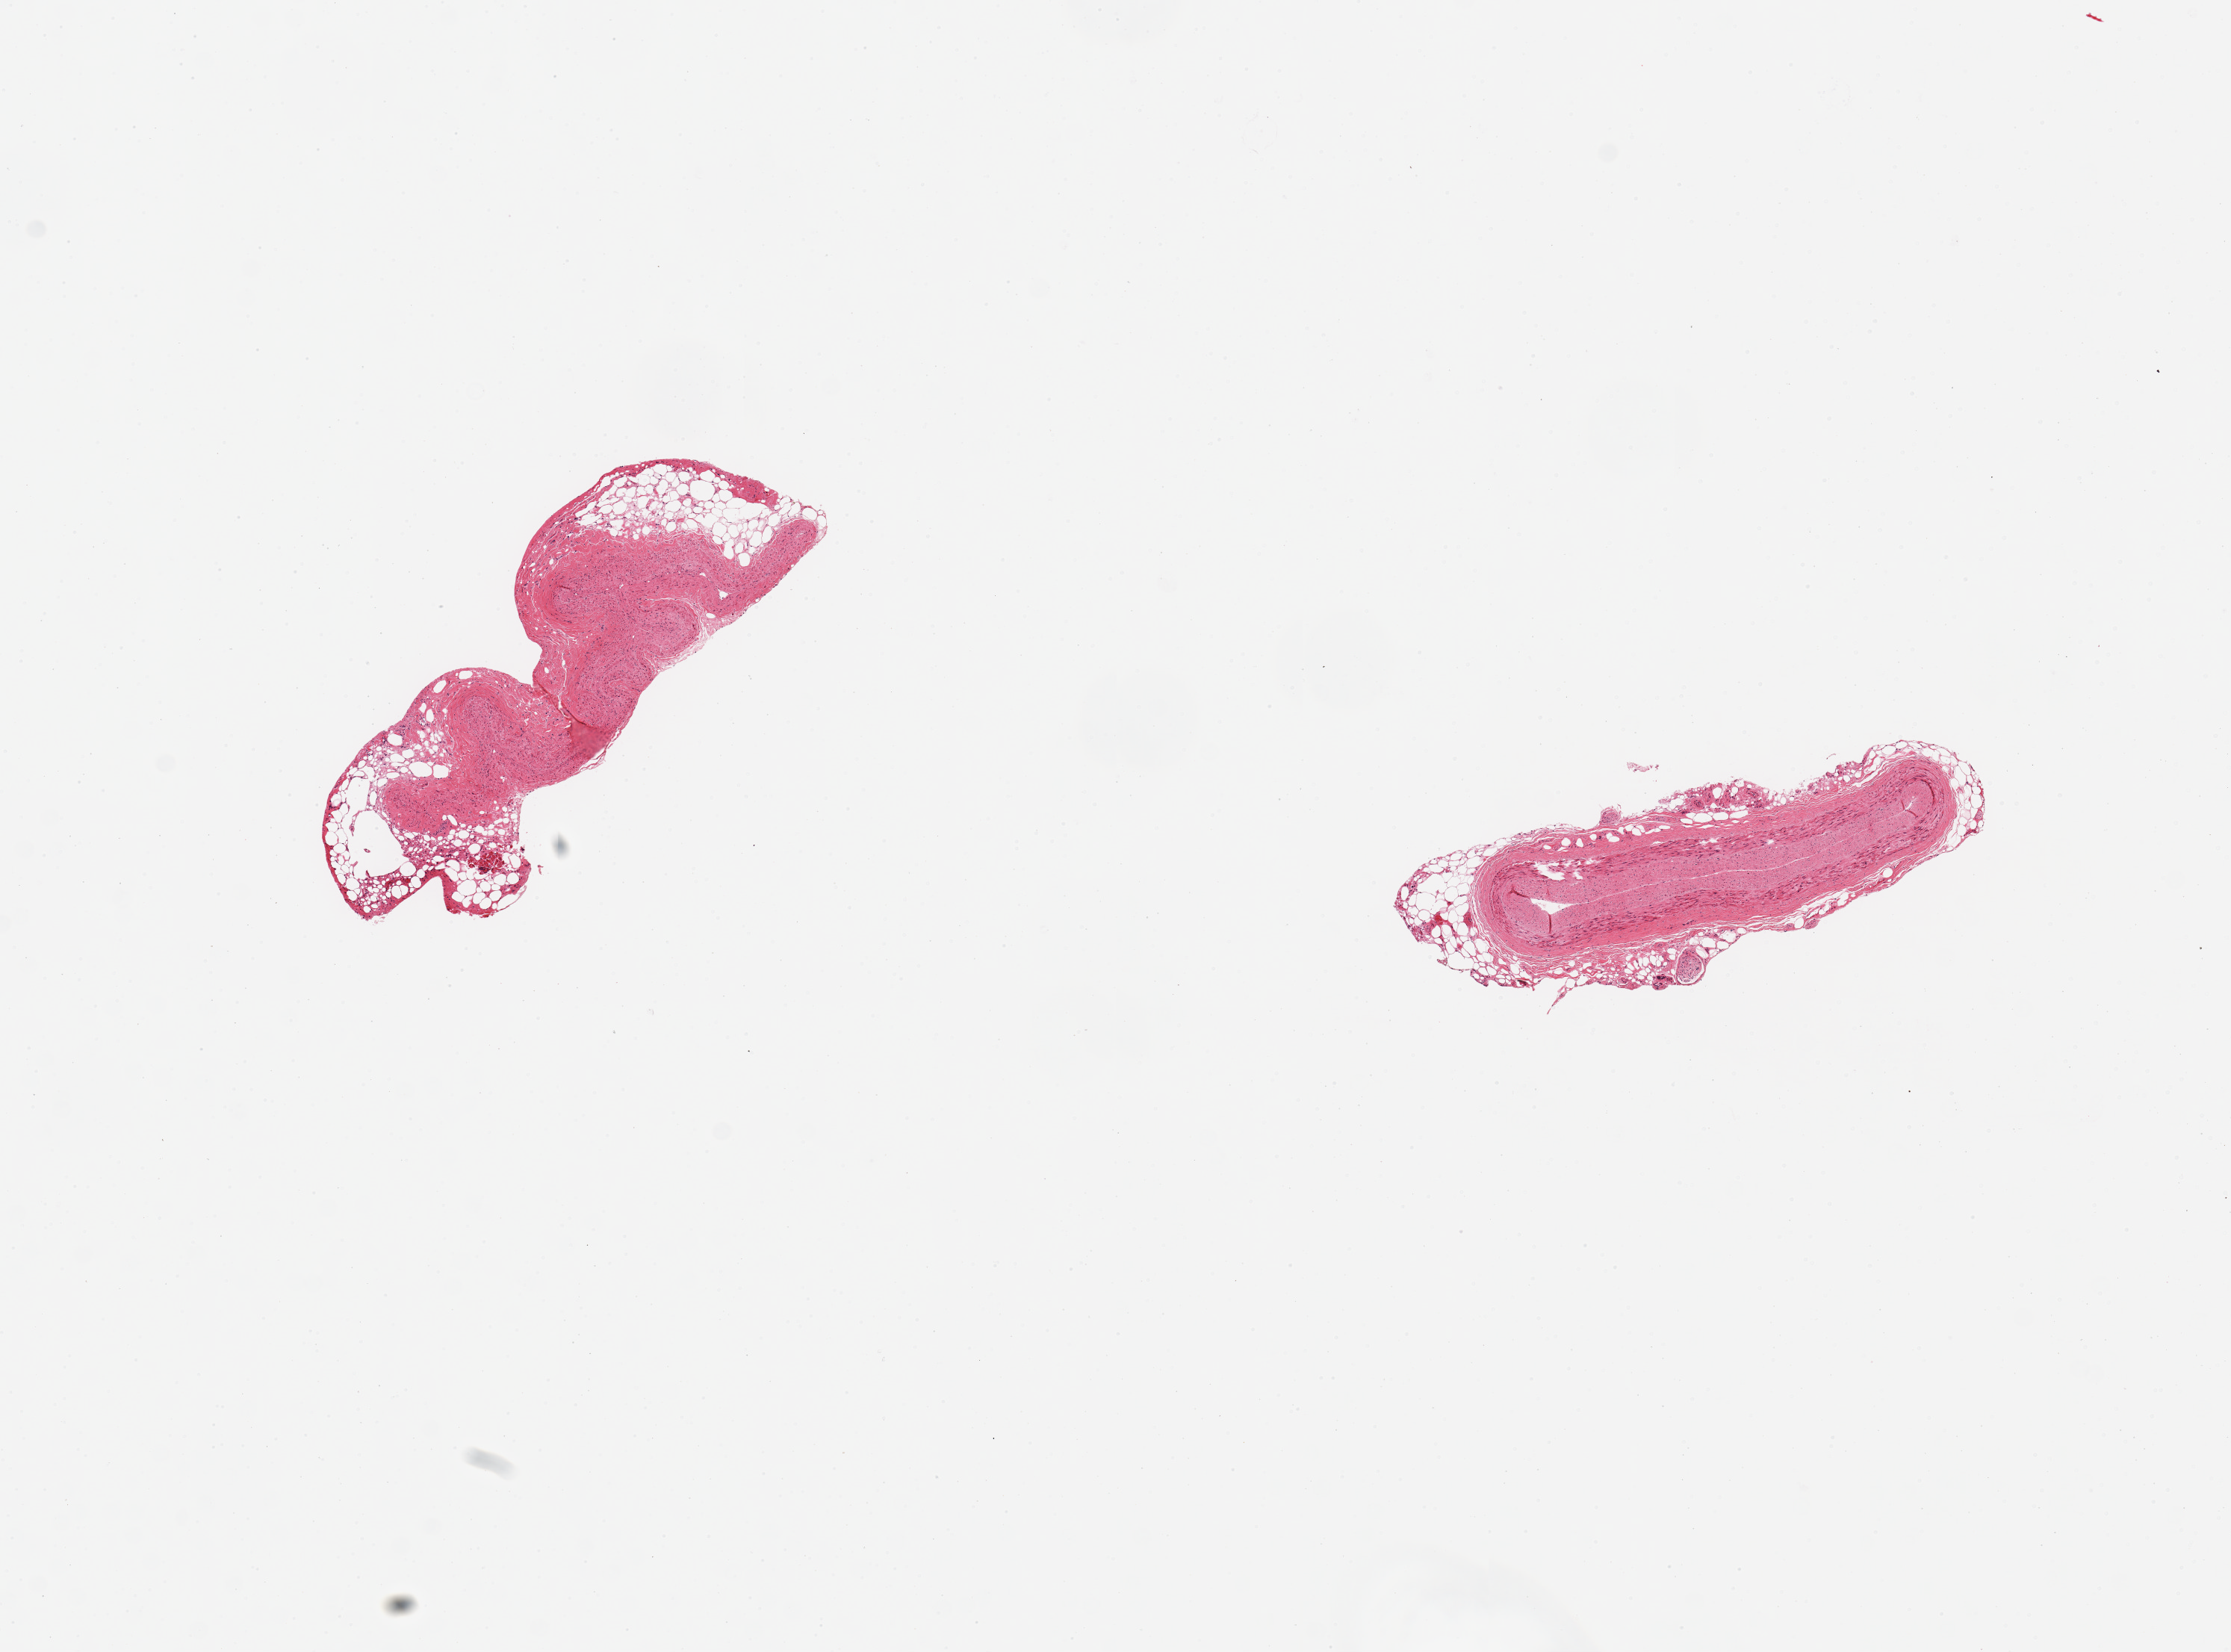
Whole-slide image, hematoxylin and eosin (H&E) stain, whole scanned area (about 11.8 x 8.7 mm) shown as a low-resolution overview, PAXgene-fixed paraffin-embedded (PFPE) section, section of coronary artery (target tissue), tissue donor sample. Donor: male.
Review note (as recorded): 2 pieces; one vein, one artery and attached fat.